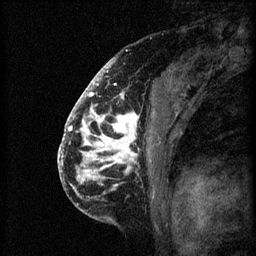
Breast MRI (dynamic contrast-enhanced), one sagittal slice. Slice 39 of 60 in the series (ordered by position). 3 images stored at this slice position (order not interpretable as contrast timing). 1.5 T. TE 4.2 ms, TR 8.2 ms. 256 × 256 image matrix. Patient: female, 41 years.
Annotated regions visible in this slice (semi-automatically segmented with operator editing):
- analysis volume of interest (the breast-tissue region the enhancement analysis was run in; not a lesion): box from (x=72, y=108) to (x=161, y=205) px
- tumour enhancement mask (voxels above the 70 % enhancement threshold inside the analysis volume of interest): (x=72, y=108)–(x=140, y=181)